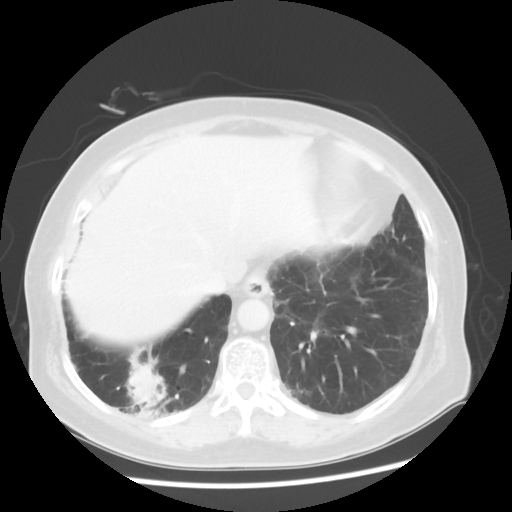
Chest CT, one axial slice. Slice 14 of 56 in the series (ordered by position). Reconstruction kernel STANDARD. 120 kVp. Lung window (W 1500 / L -600 HU). 512 × 512 image matrix. Patient: female, 64 years. Case-level facts recorded for this patient, not image findings: clinical TNM (as recorded): Tis N0 M0.
Outlined on this slice (bounding box drawn by a radiologist):
- lung tumour (recorded histology: adenocarcinoma): box from (x=120, y=345) to (x=180, y=428) px